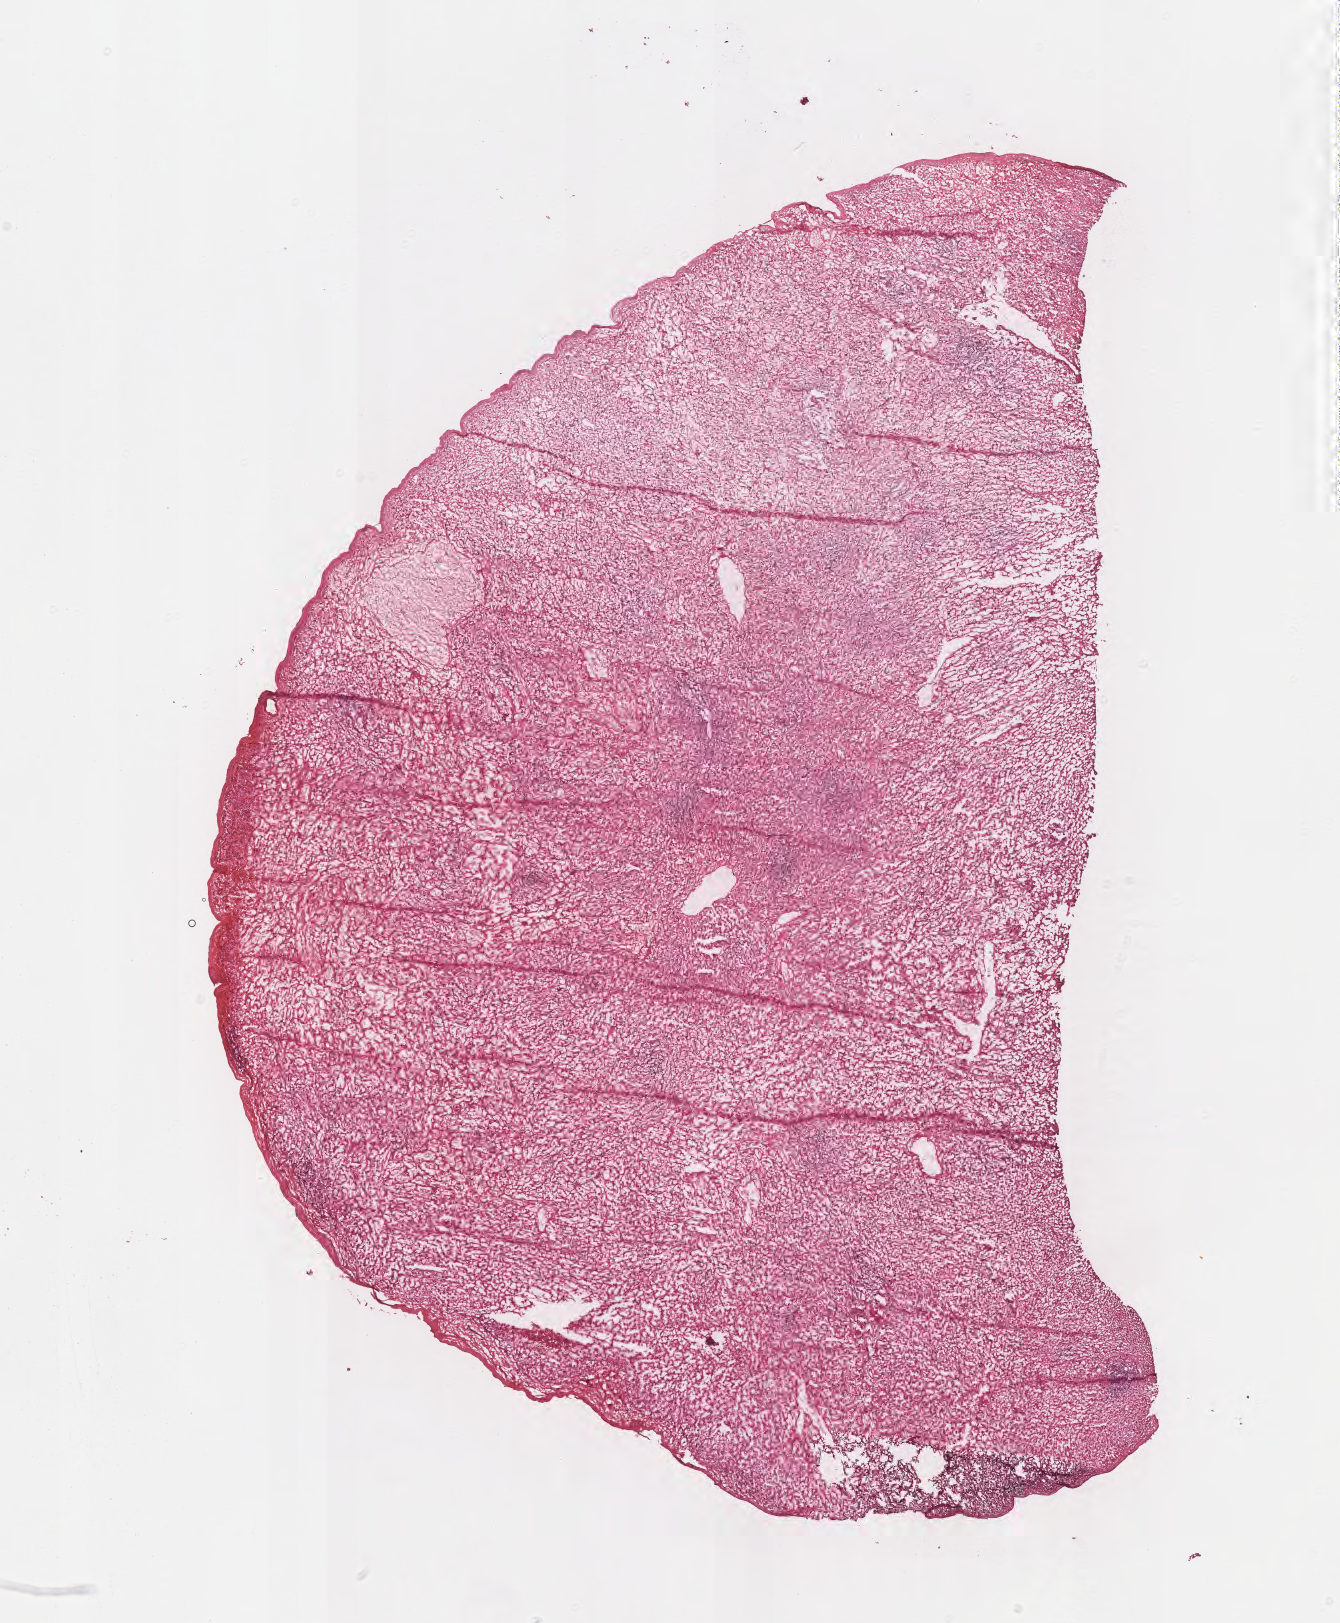
Whole-slide image, H&E stain — low-resolution overview of the scanned area, about 10.6 x 12.8 mm; frozen section; non-tumor (normal tissue) sample from a patient with adenocarcinoma, NOS; anatomic site: colon. Male, age 69 years at initial diagnosis. Pathologist review of this section (percent, as recorded): tumor cells 0%, tumor nuclei 0%, stromal cells 99%, necrosis 0%, normal cells 11%. Inflammatory infiltration, as recorded: lymphocyte infiltration 78%, monocyte infiltration 2%, neutrophil infiltration 0%.
- this section: non-tumor tissue sample; the patient's diagnosis is given above